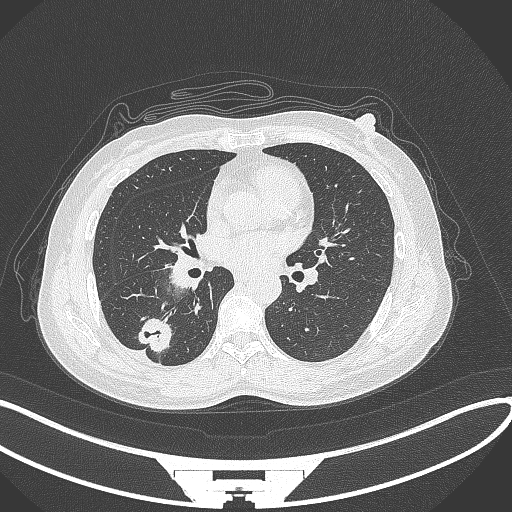
Chest CT, one axial slice; position 148 of 352 along the scan axis; reconstruction kernel B70f; lung window (W 1500 / L -600 HU); 512 × 512 image matrix, field of view 400 × 400 mm. Female patient, age 55 years. Case-level facts recorded for this patient, not image findings: clinical TNM (as recorded): T1c N1 M0.
Structures marked on this image (rectangle marked by the reading radiologist):
- lung tumour (recorded histology: adenocarcinoma): bounding box [x1, y1, x2, y2] px = [134, 315, 178, 356]